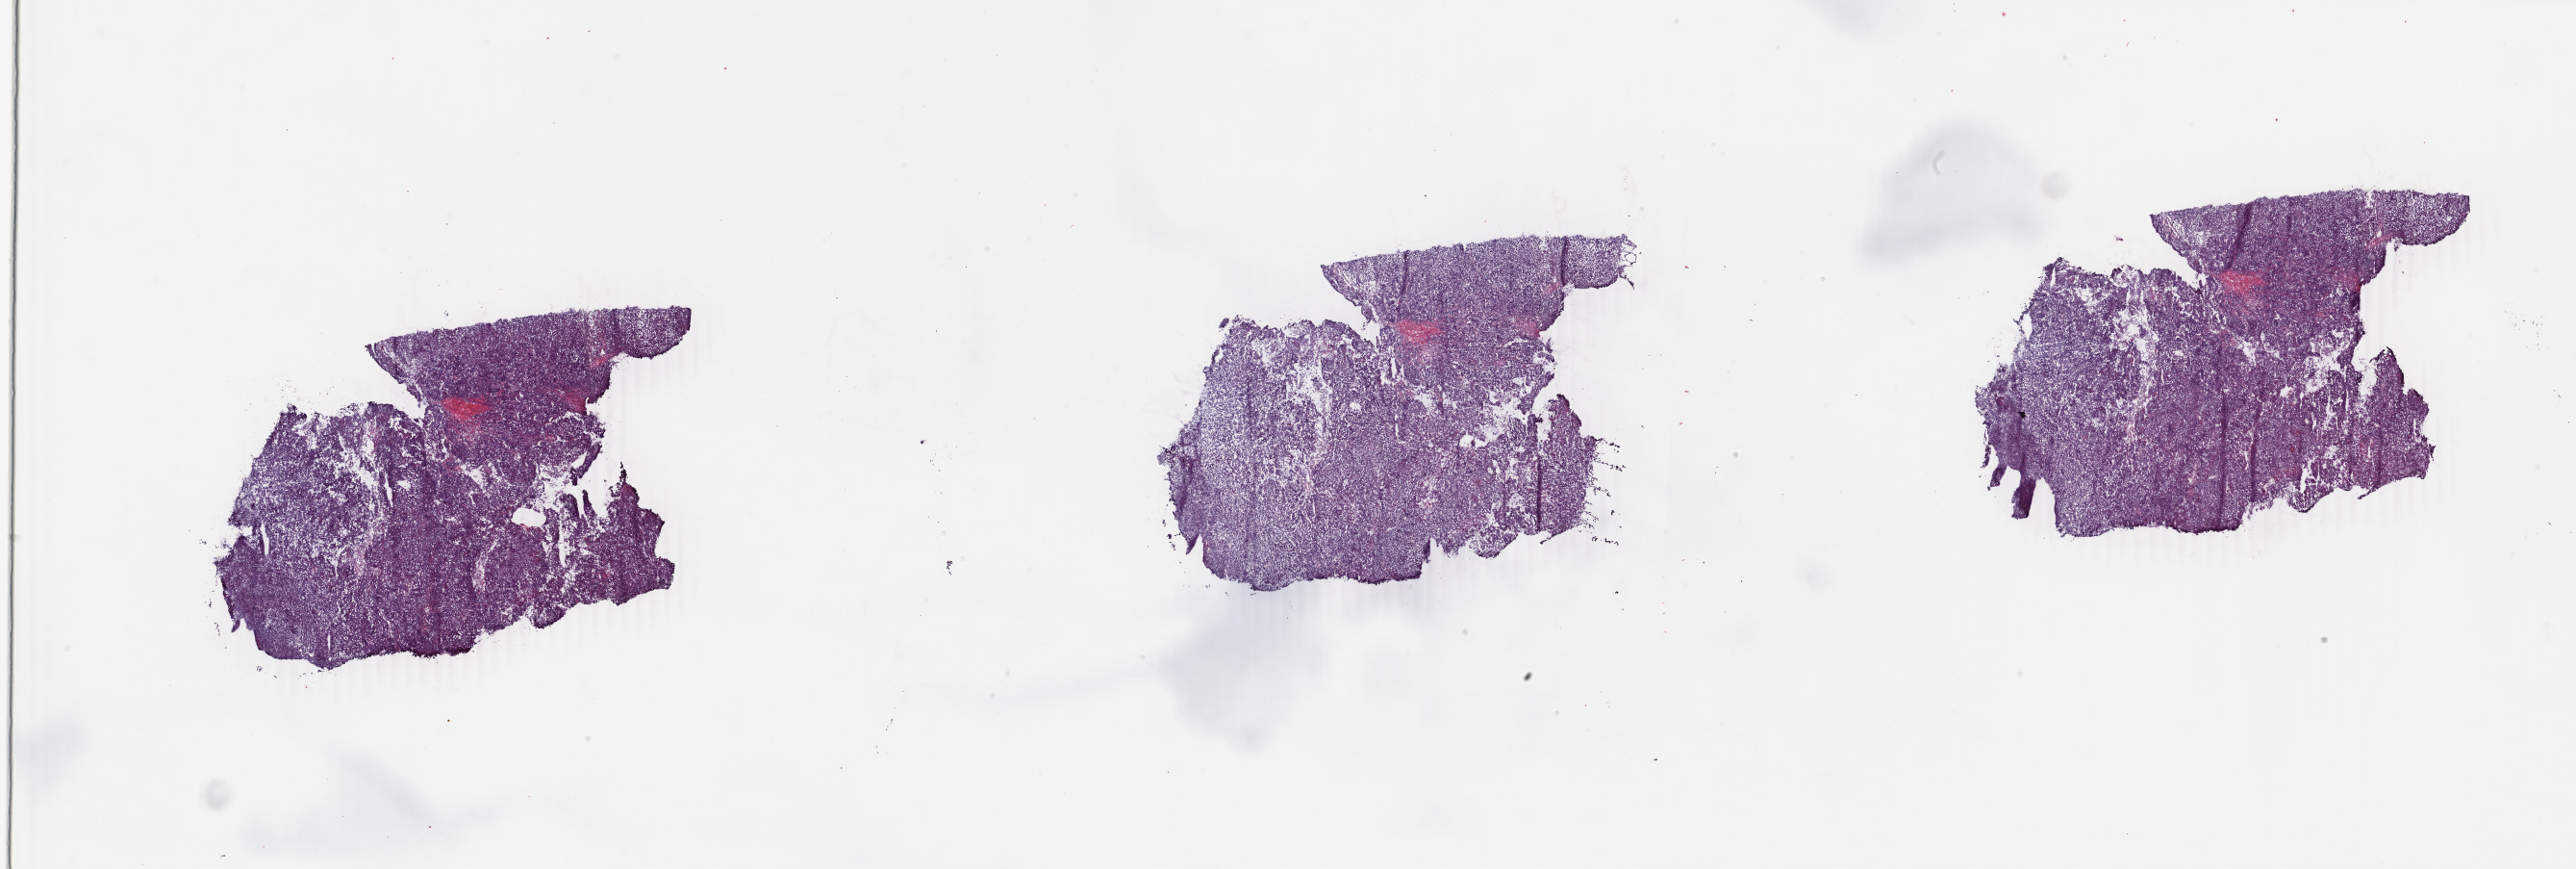
H&E whole-slide image, shown as a low-resolution overview of the whole scanned area (about 42.6 x 14.4 mm, from a 40x scan); frozen section from the bottom of the tissue portion; breast, primary tumour sample. Female, age 61 years at initial diagnosis. Composition of this section per pathologist review: tumour cells 95%, tumour nuclei 95%, normal cells 0%, stromal cells 5%, necrosis 0%. Infiltration values recorded for this section: lymphocyte infiltration 0%, monocyte infiltration 0%, neutrophil infiltration 0%.
AJCC pathologic stage: IIA. Pathologic diagnosis: Infiltrating duct carcinoma, NOS. Lymph nodes positive (case pathology): 0 of 4 examined.